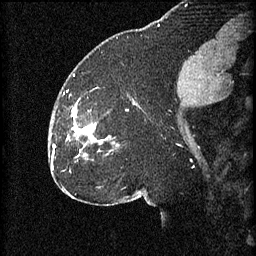
Breast MRI (dynamic contrast-enhanced), one sagittal slice. Position 31 of 60 along the scan axis. 3 images stored at this slice position (order not interpretable as contrast timing). 1.5 T. TE 4.2 ms, TR 8.2 ms. 256 × 256 image matrix, field of view 180 × 180 mm. Patient: female, 32 years.
Annotated regions visible in this slice (semi-automatic segmentation, software-assisted and operator-edited):
- analysis volume of interest (the breast-tissue region the enhancement analysis was run in; not a lesion): bounding box <67,106,111,159> (left, top, right, bottom; pixels)
- tumour enhancement mask (voxels above the 70 % enhancement threshold inside the analysis volume of interest): <68,110,96,139>